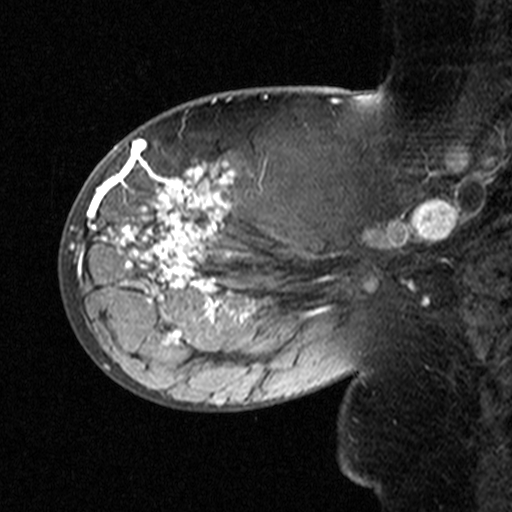
Breast MRI (dynamic contrast-enhanced), one sagittal slice. Slice 18 of 44 in the series (ordered by position). Dynamic contrast-enhanced study with each time point stored as its own series, time point 2 of 3 at this slice position (early post-contrast, ordered by acquisition time). 1.5 T. TE 4.5 ms, TR 11 ms. 3 mm slice thickness. 512 × 512 image matrix. Female patient, age 53 years. Case-level facts recorded for this patient, not image findings: setting: breast cancer imaged before/during neoadjuvant chemotherapy; receptor status: HR-positive, HER2-negative.
Outlined on this slice (semi-automatic segmentation, software-assisted and operator-edited):
- analysis volume of interest (the breast-tissue region the enhancement analysis was run in; not a lesion): bounding box (x1, y1, x2, y2) in pixels: (76, 140, 311, 353)
- tumour enhancement mask (voxels above the 90 % enhancement threshold inside the analysis volume of interest): (76, 160, 310, 344)